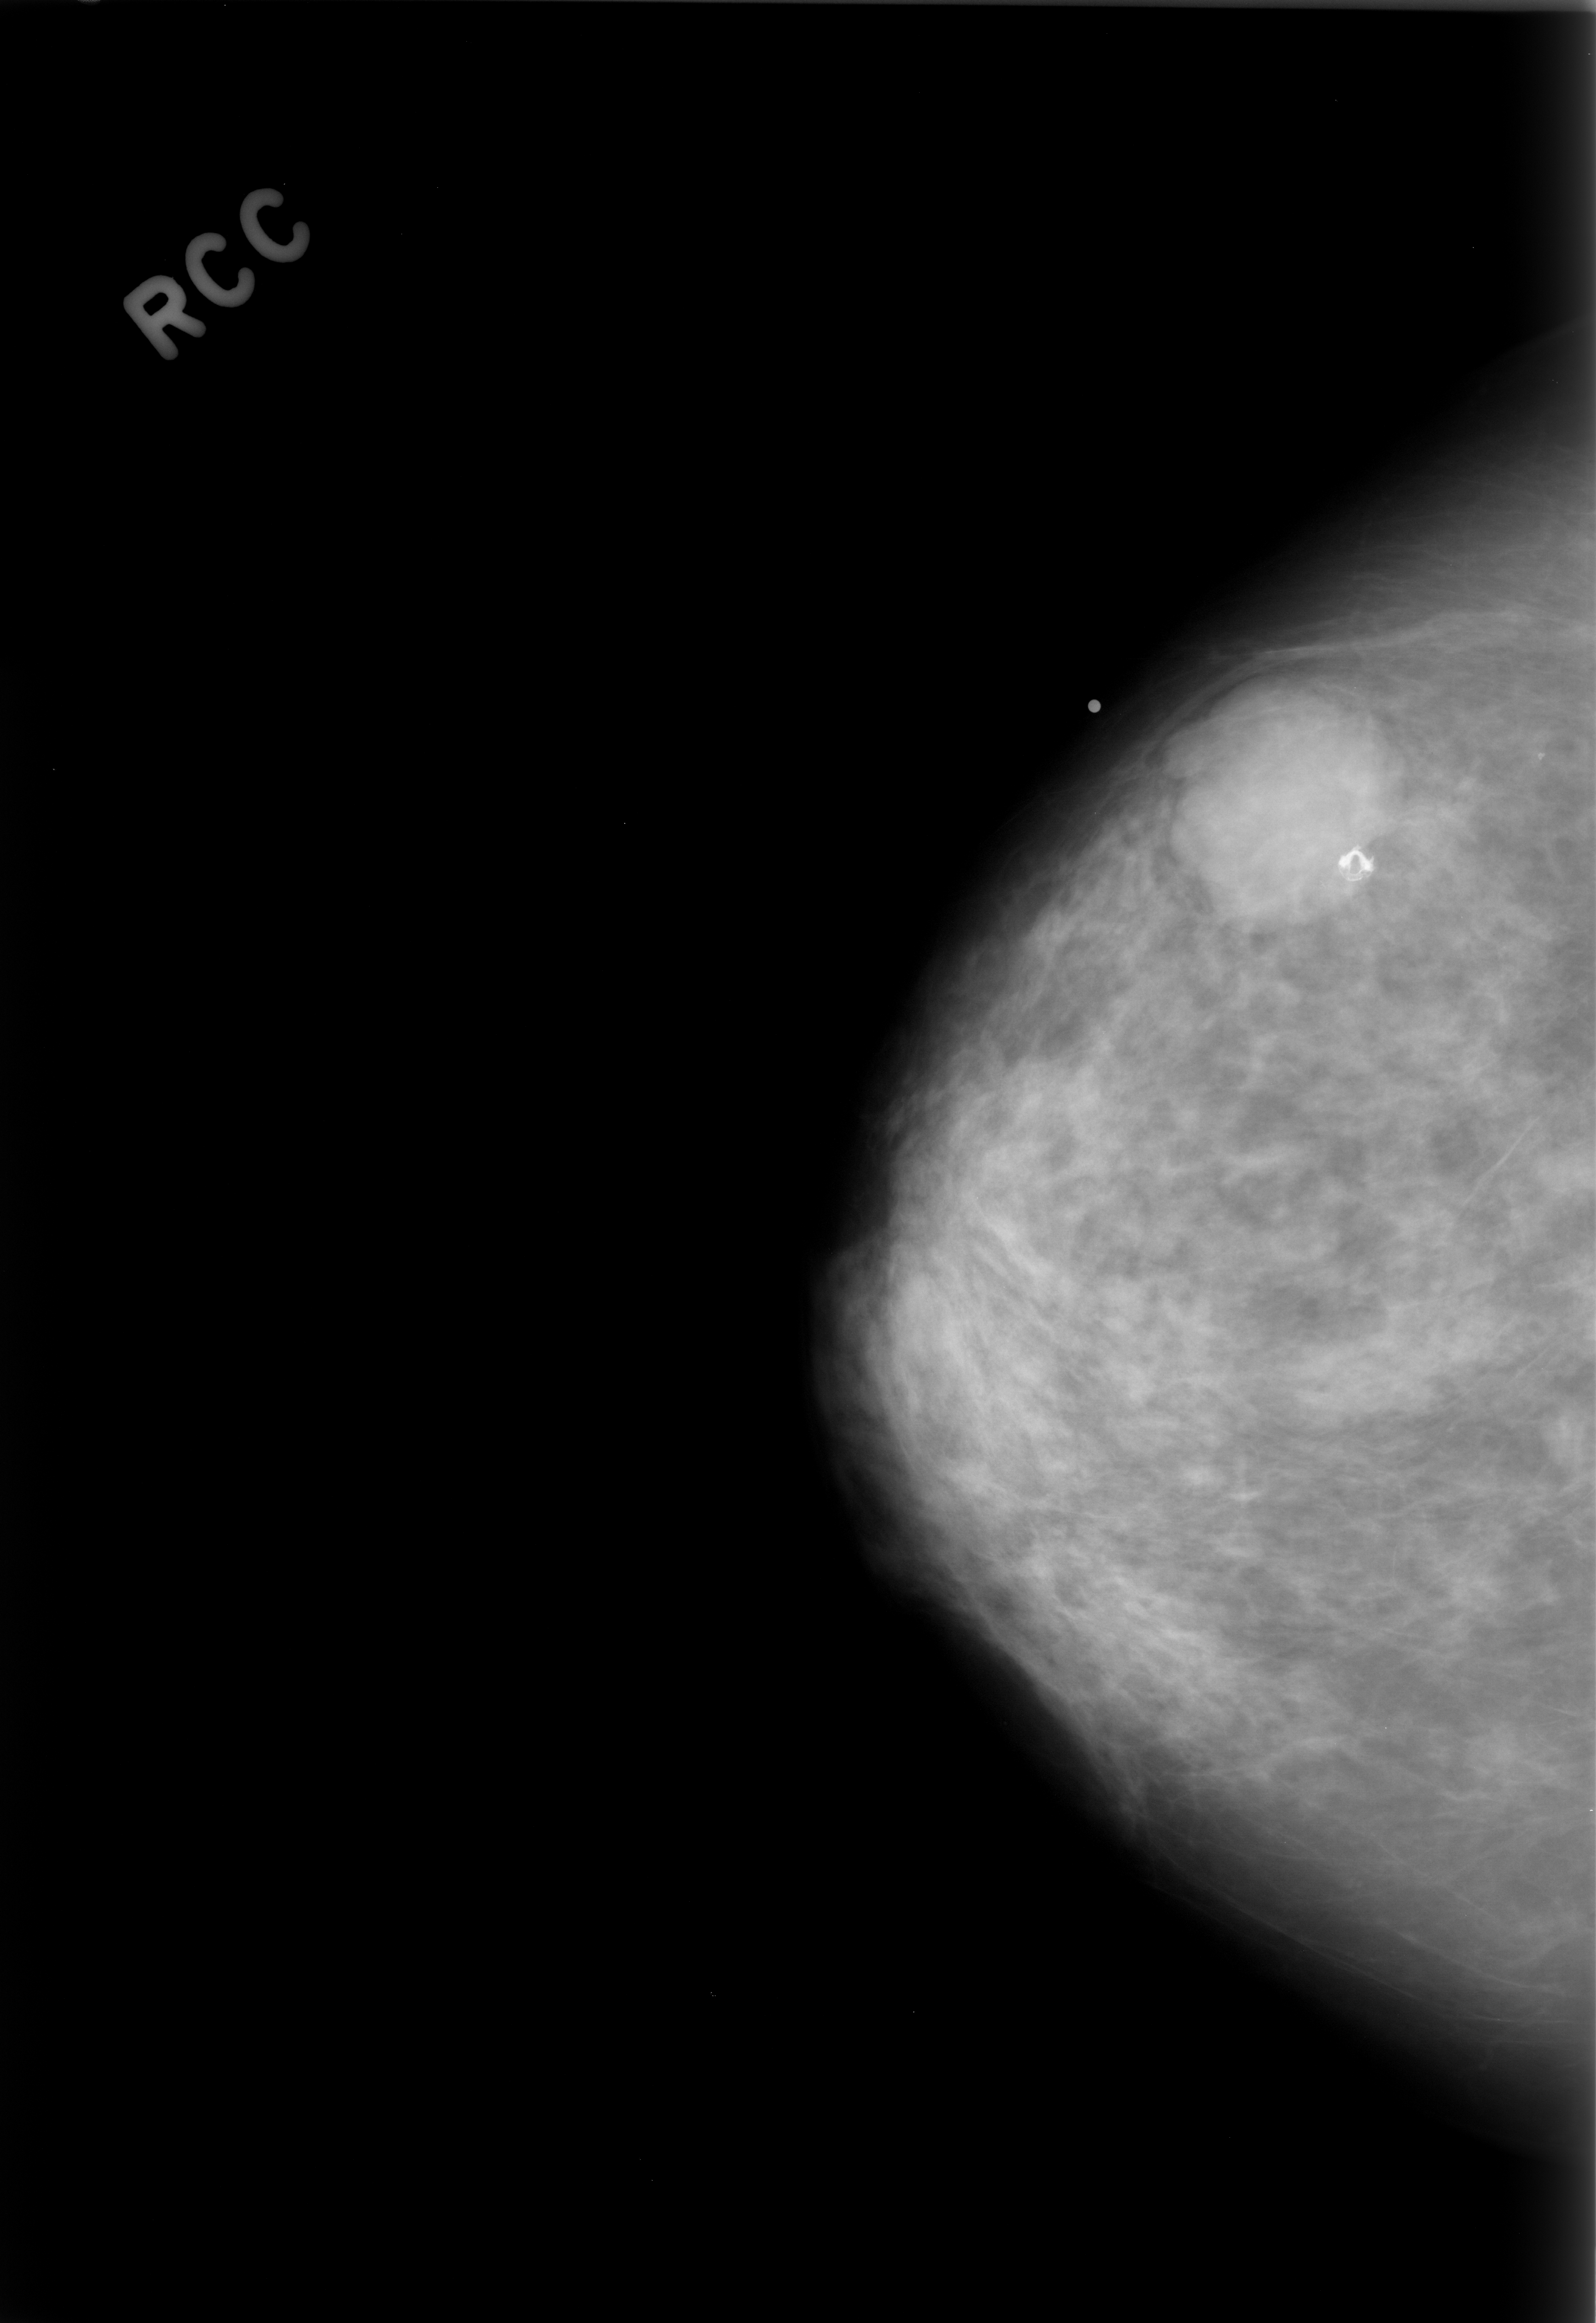
Digitized screen-film mammogram; right breast; craniocaudal (CC) view.
Finding: mass, shape round, margins microlobulated; BI-RADS assessment category 4; pathology result (as recorded, not read from the image): benign.